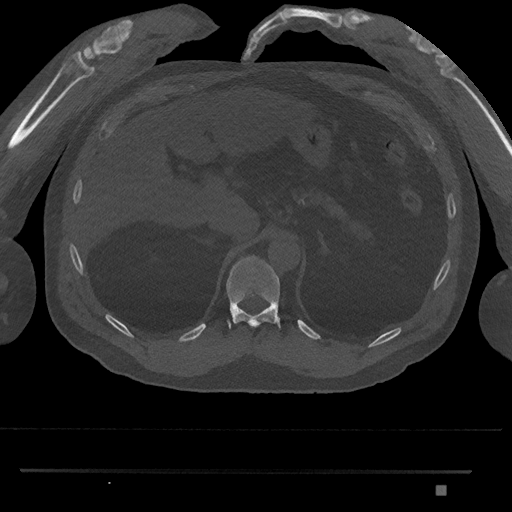
CT including the spine, one axial slice; reconstruction kernel Br40s/3; 120 kVp; bone window (W 1800 / L 400 HU); 0.5 mm slice thickness; 512 × 512 image matrix, field of view 429 × 429 mm. Male patient, age 65 years. From the clinical record (not read from this slice): primary cancer: prostate.
Annotated regions visible in this slice (semi-automatically segmented with operator editing):
- T11 vertebra: bounding box [x1, y1, x2, y2] px = [226, 256, 281, 329]